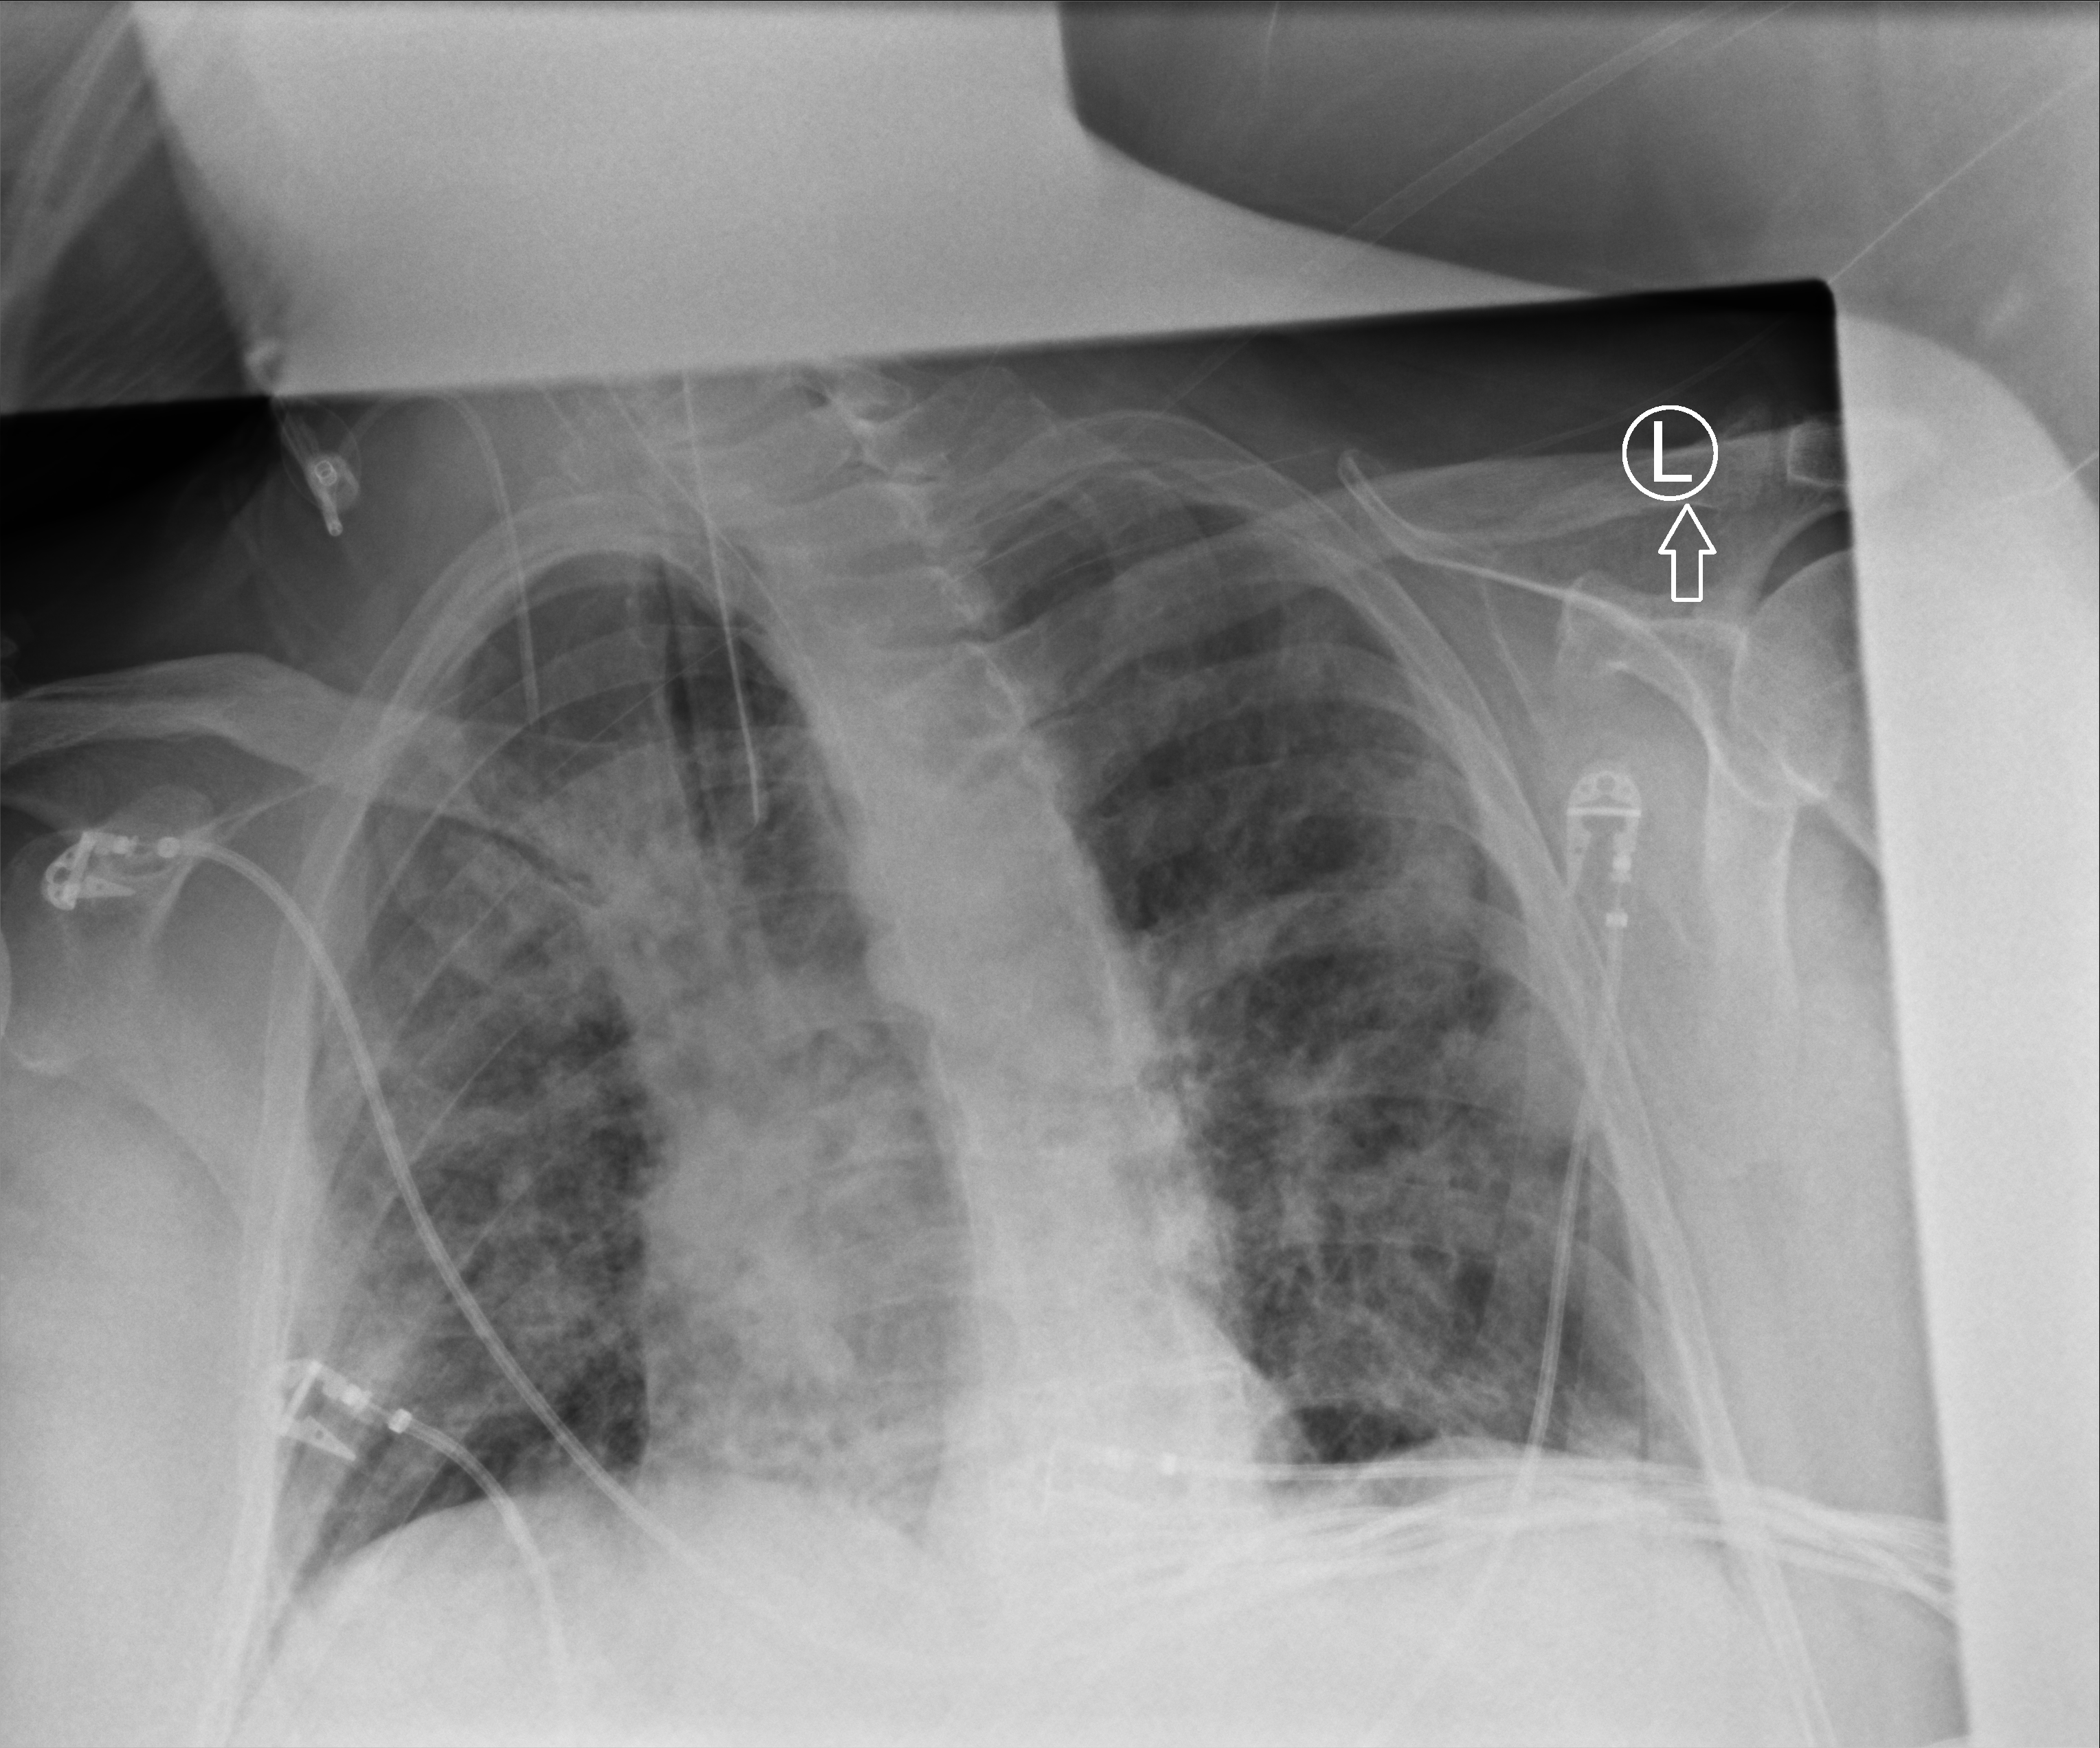
Chest X-ray (portable), anteroposterior (AP) projection. Patient hospitalised with COVID-19; male, aged 60–74 years.
Admission-level facts for this patient (not findings on this image; timing relative to this image not recorded): diabetes (admission record): yes; mechanically ventilated during this hospital stay: yes; admitted to intensive care during this hospital stay: yes.